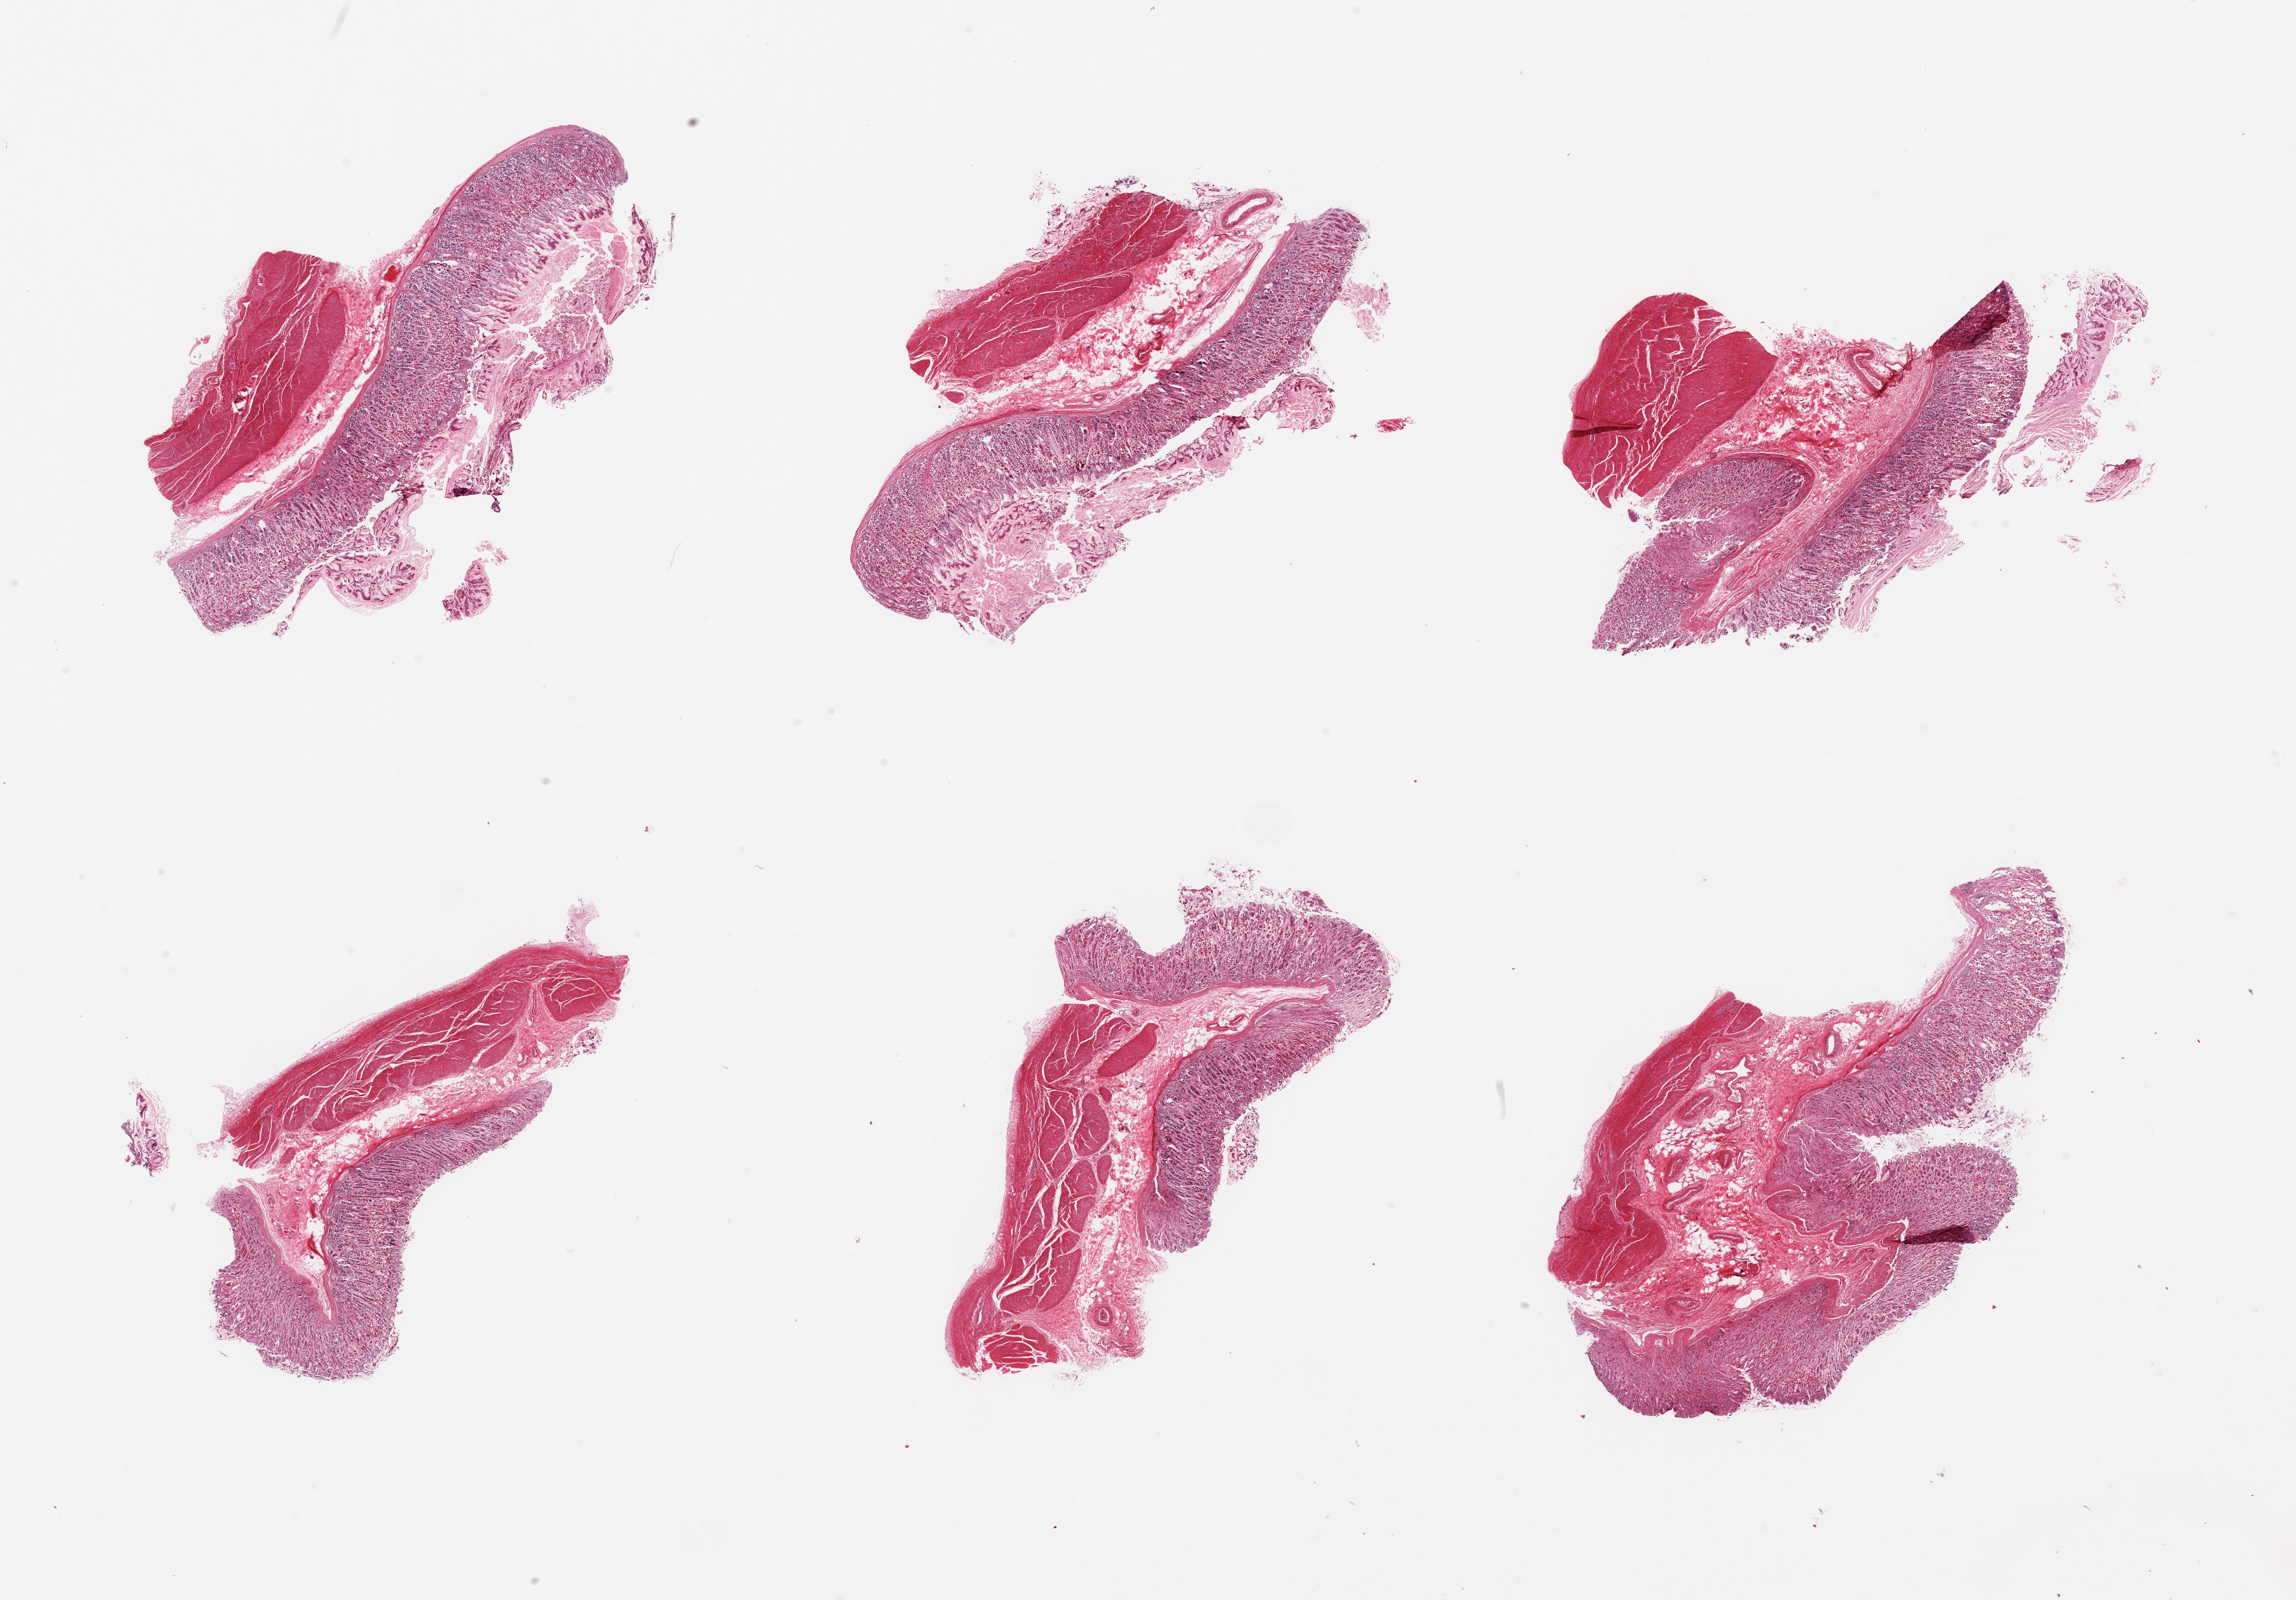
Hematoxylin and eosin (H&E) whole-slide image, brightfield, low-resolution overview of the scanned area, about 28.5 x 19.9 mm. PAXgene-fixed paraffin-embedded (PFPE) section. Section of stomach (target tissue). Donor tissue sample.
• pathologist's review note for this sample: 6 pieces, mucosa up to ~1.3mm, ~40-50% thickness, moderately advanced autolysis